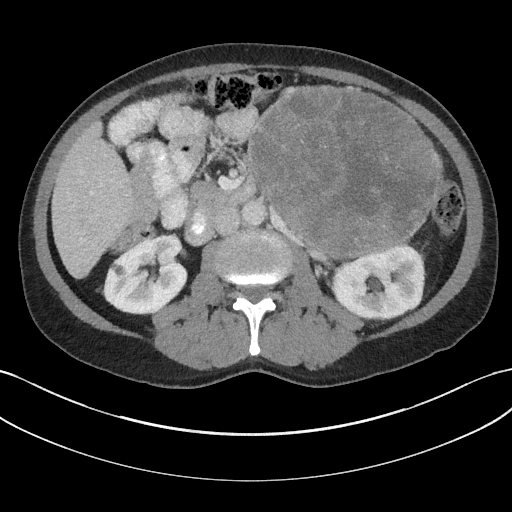
Contrast-enhanced abdominal CT, one axial slice. Reconstruction kernel I31f/3. 100 kVp. Intravenous contrast given. Soft-tissue window (W 400 / L 40 HU). 3 mm slice thickness. 512 × 512 image matrix. Patient: male, 58 years. Case-level facts recorded for this patient, not image findings: diagnosis: adrenocortical carcinoma; tumour side: left adrenal; tumour size at pathology: 22 cm; Ki-67 index: 26 %; stage (as recorded): 2.
Outlined on this slice (semi-automatically segmented with operator editing):
- mass: bounding box (x1, y1, x2, y2) in pixels: (251, 87, 437, 257)